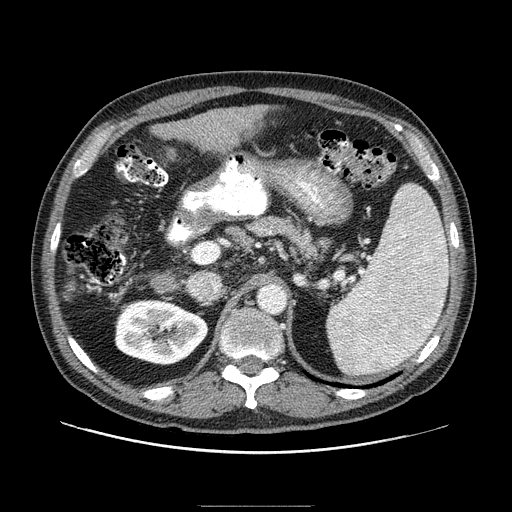
Contrast-enhanced abdominal CT (liver protocol), one axial slice. Position 44 of 99 along the scan axis. 100 kVp. One of 2 acquisitions stored at this slice position. Soft-tissue window (W 400 / L 40 HU). 2.5 mm slice thickness. 512 × 512 image matrix, field of view 400 × 400 mm. Case-level facts recorded for this patient, not image findings: diagnosis: hepatocellular carcinoma (patient treated with transarterial chemoembolisation; whether this scan precedes or follows treatment is not stated here); TNM stage (as recorded): Stage-II; Child-Pugh class: A; tumour differentiation: well differentiated; tumour nodularity: multinodular.
Outlined on this slice (semi-automatically segmented with operator editing):
- liver parenchyma outside the tumour (the mass and vessels are separate outlines, so this box may not span the whole liver): bounding box <179,104,268,151> (left, top, right, bottom; pixels)